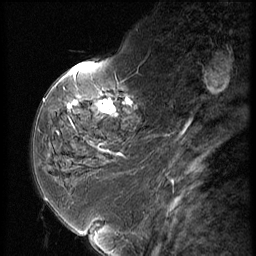
Breast MRI (dynamic contrast-enhanced), one sagittal slice. Slice 18 of 56 in the series (ordered by position). Dynamic contrast-enhanced series, image 2 of 3 at this slice position (ordered by acquisition). 1.5 T. TE 4.2 ms, TR 9 ms. 2.5 mm slice thickness. 256 × 256 image matrix. Patient: female, 59 years. From the clinical record (not read from this slice): setting: breast cancer imaged before/during neoadjuvant chemotherapy; receptor status: HER2-positive.
Outlined on this slice (semi-automatic segmentation, software-assisted and operator-edited):
- analysis volume of interest (the breast-tissue region the enhancement analysis was run in; not a lesion): bounding box (x1, y1, x2, y2) in pixels: (44, 66, 151, 135)
- tumour enhancement mask (voxels above the 140 % enhancement threshold inside the analysis volume of interest): (67, 97, 131, 117)